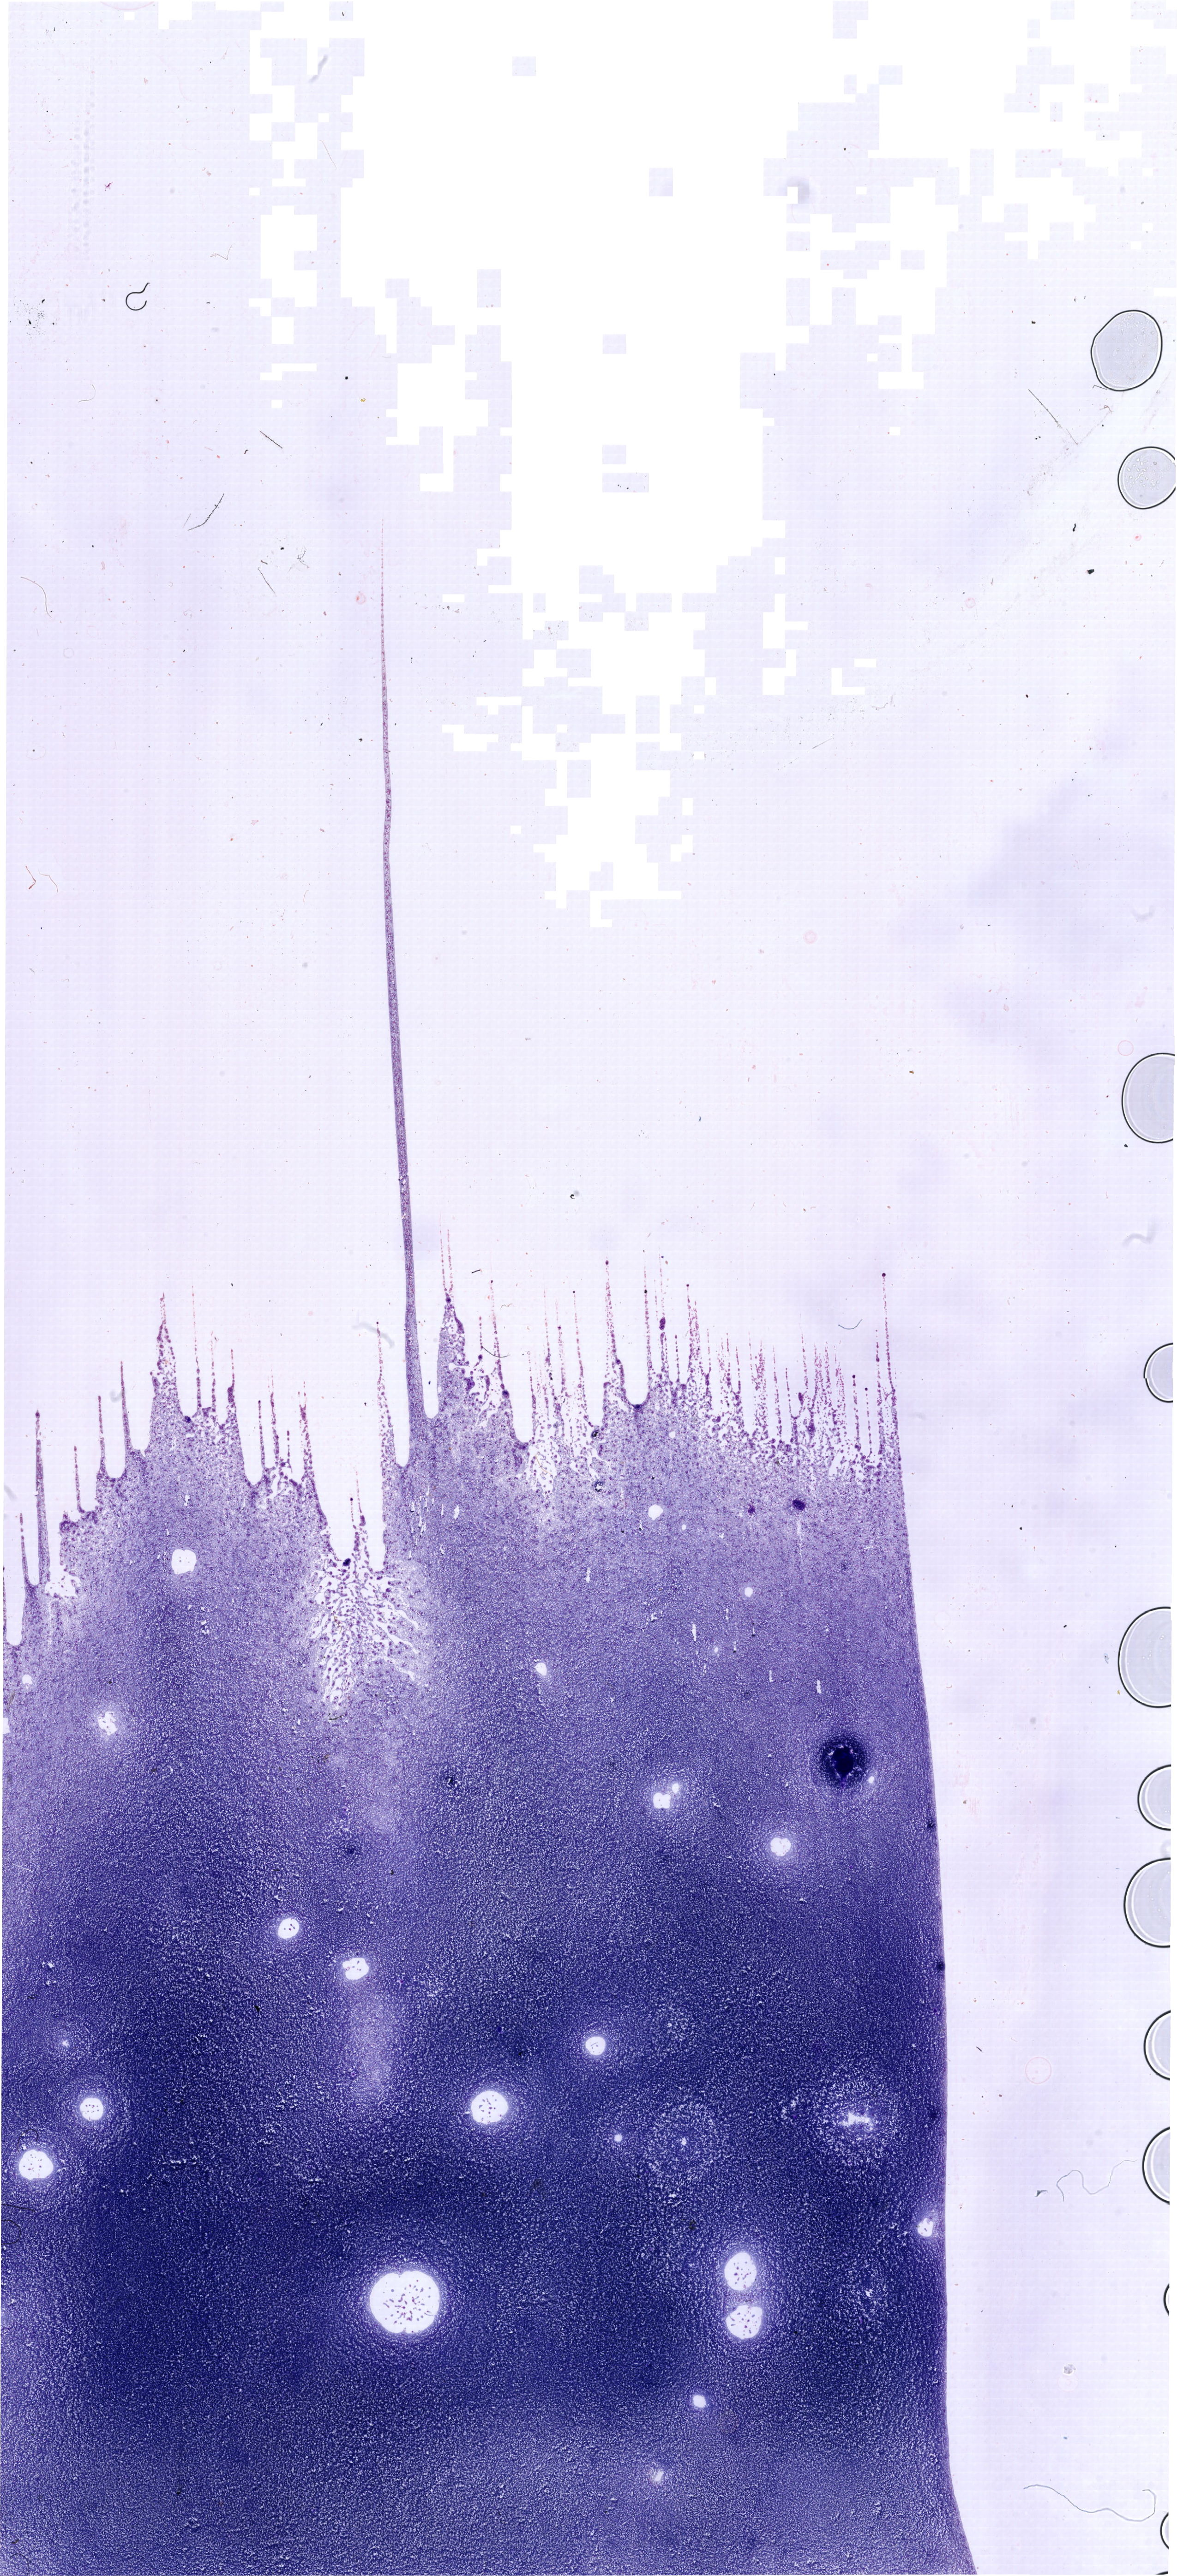
Whole-slide image of a May-Grünwald–Giemsa-stained bone marrow aspirate smear, shown as a low-resolution overview of the whole scanned area (about 19.9 x 43.6 mm). Patient sex: female.
Diagnosis: T Acute Lymphoblastic Leukemia.